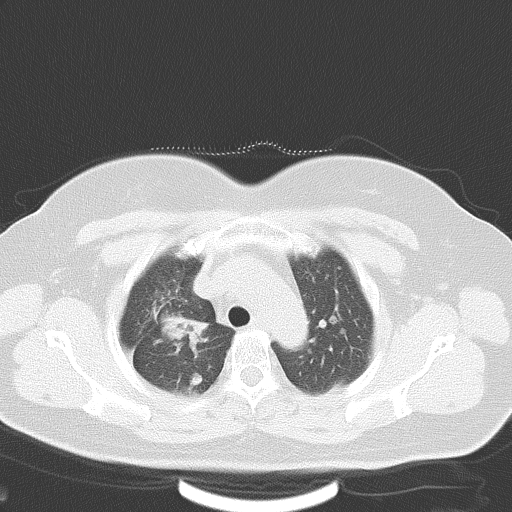
Chest CT, one axial slice; slice 39 of 48 in the series (ordered by position); 120 kVp; lung window (W 1500 / L -600 HU); 512 × 512 image matrix, field of view 353 × 353 mm. Female patient, age 50 years. From the clinical record (not read from this slice): clinical TNM (as recorded): T2a N0 M1a.
Structures marked on this image (bounding box drawn by a radiologist):
- lung tumour (recorded histology: adenocarcinoma): bounding box (x1, y1, x2, y2) in pixels: (149, 303, 213, 356)